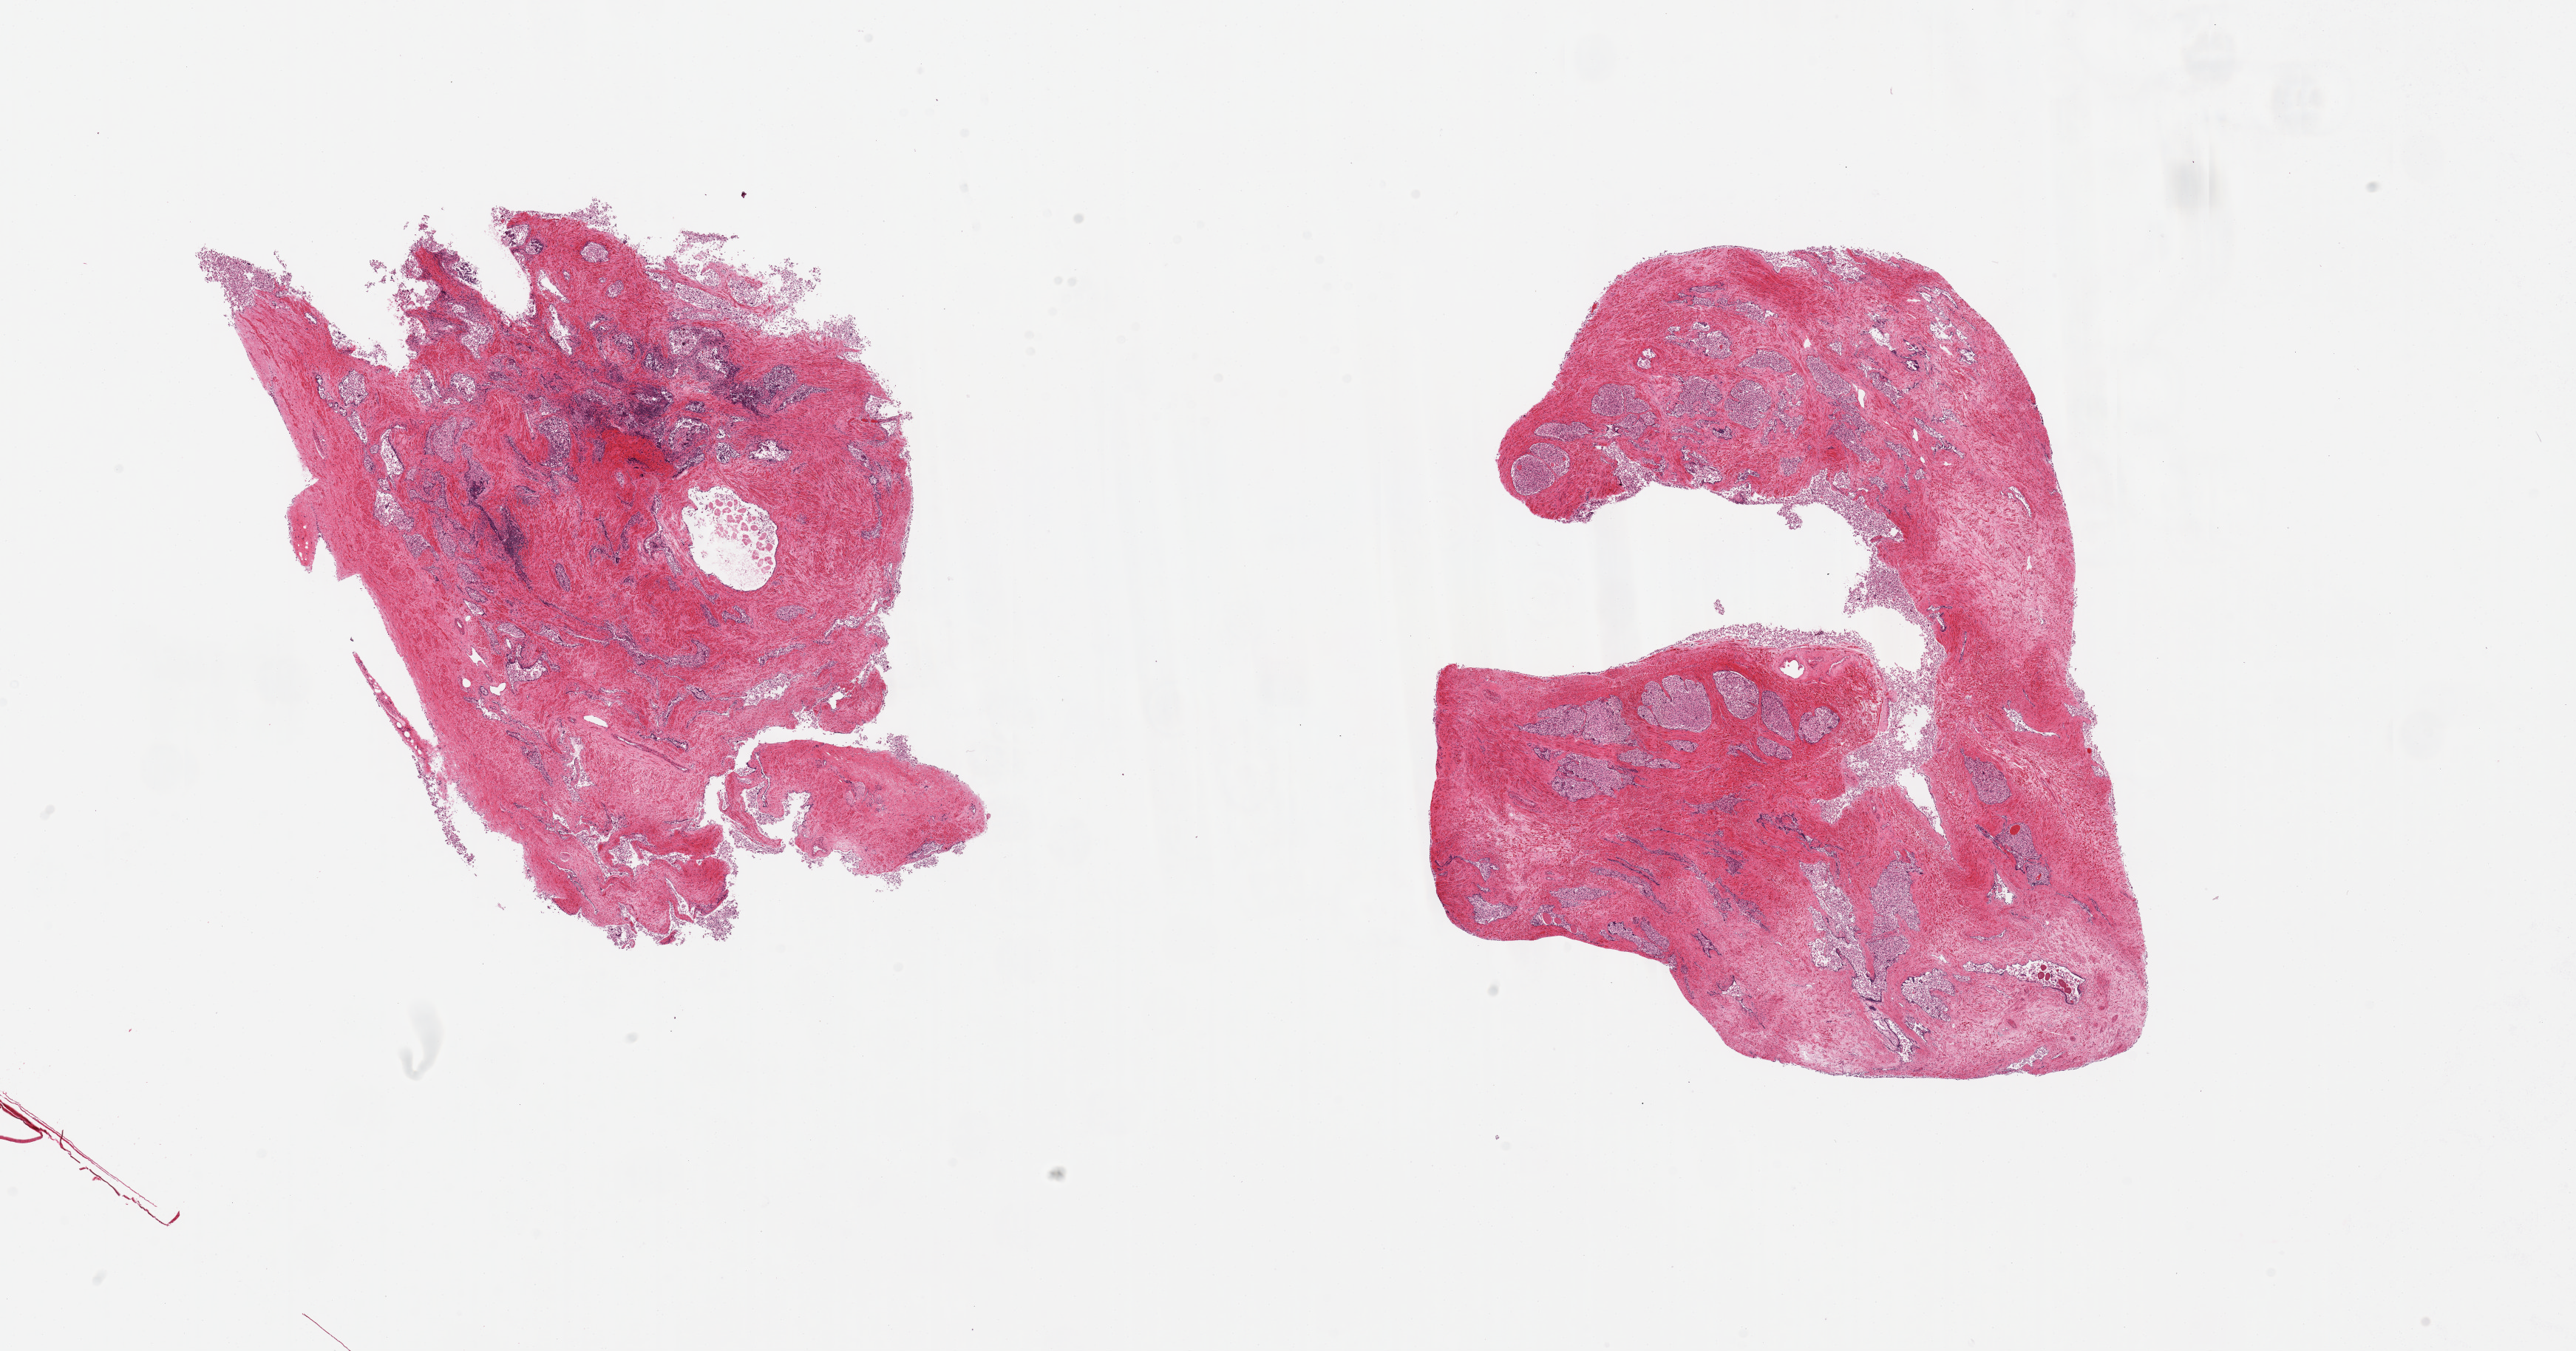
Whole-slide image, hematoxylin and eosin (H&E) stain — whole scanned area (about 27.6 x 14.5 mm, from a 20x scan) shown as a low-resolution overview, PAXgene-fixed paraffin-embedded (PFPE) section, section of prostate (target tissue), tissue donor sample. Male donor.
Pathologist's review note for this sample: 2 pieces; glands totally autolyzed; stroma intact.